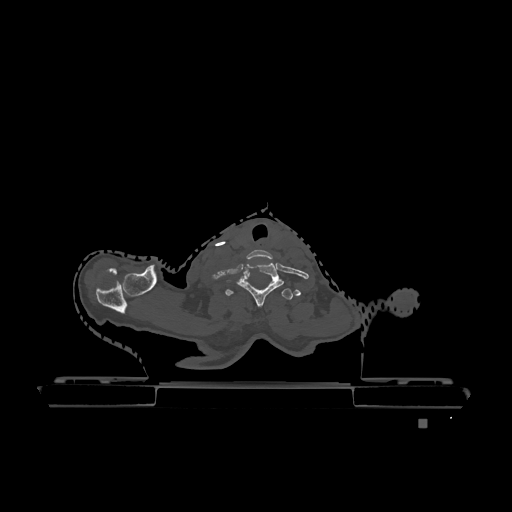
CT including the spine, one axial slice; slice 1024 of 1317 in the series (ordered by position); bone window (W 1800 / L 400 HU); 0.5 mm slice thickness; 512 × 512 image matrix. Patient: female, 74 years. Case-level facts recorded for this patient, not image findings: primary cancer: lung; vertebrae with lytic lesions (as recorded): T1, T4, T5, T6, L4, L5.
Structures marked on this image (semi-automatic segmentation, software-assisted and operator-edited):
- T1 vertebra: bounding box [x1, y1, x2, y2] px = [225, 289, 293, 300]